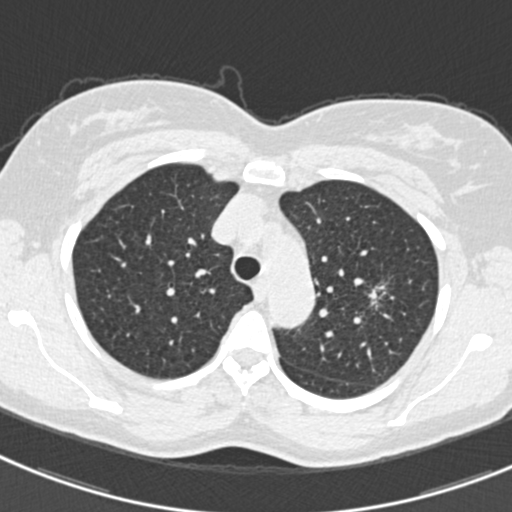
Low-dose screening chest CT, one axial slice; slice 241 of 309 in the series (ordered by position); reconstruction kernel B30f; lung window (W 1500 / L -600 HU); 1 mm slice thickness; 512 × 512 image matrix, field of view 302 × 302 mm.
Annotated regions visible in this slice (outlined manually by an expert reader):
- lesion 1 (tumor, upper lobe of left lung): bounding box (x1, y1, x2, y2) in pixels: (369, 289, 379, 303)